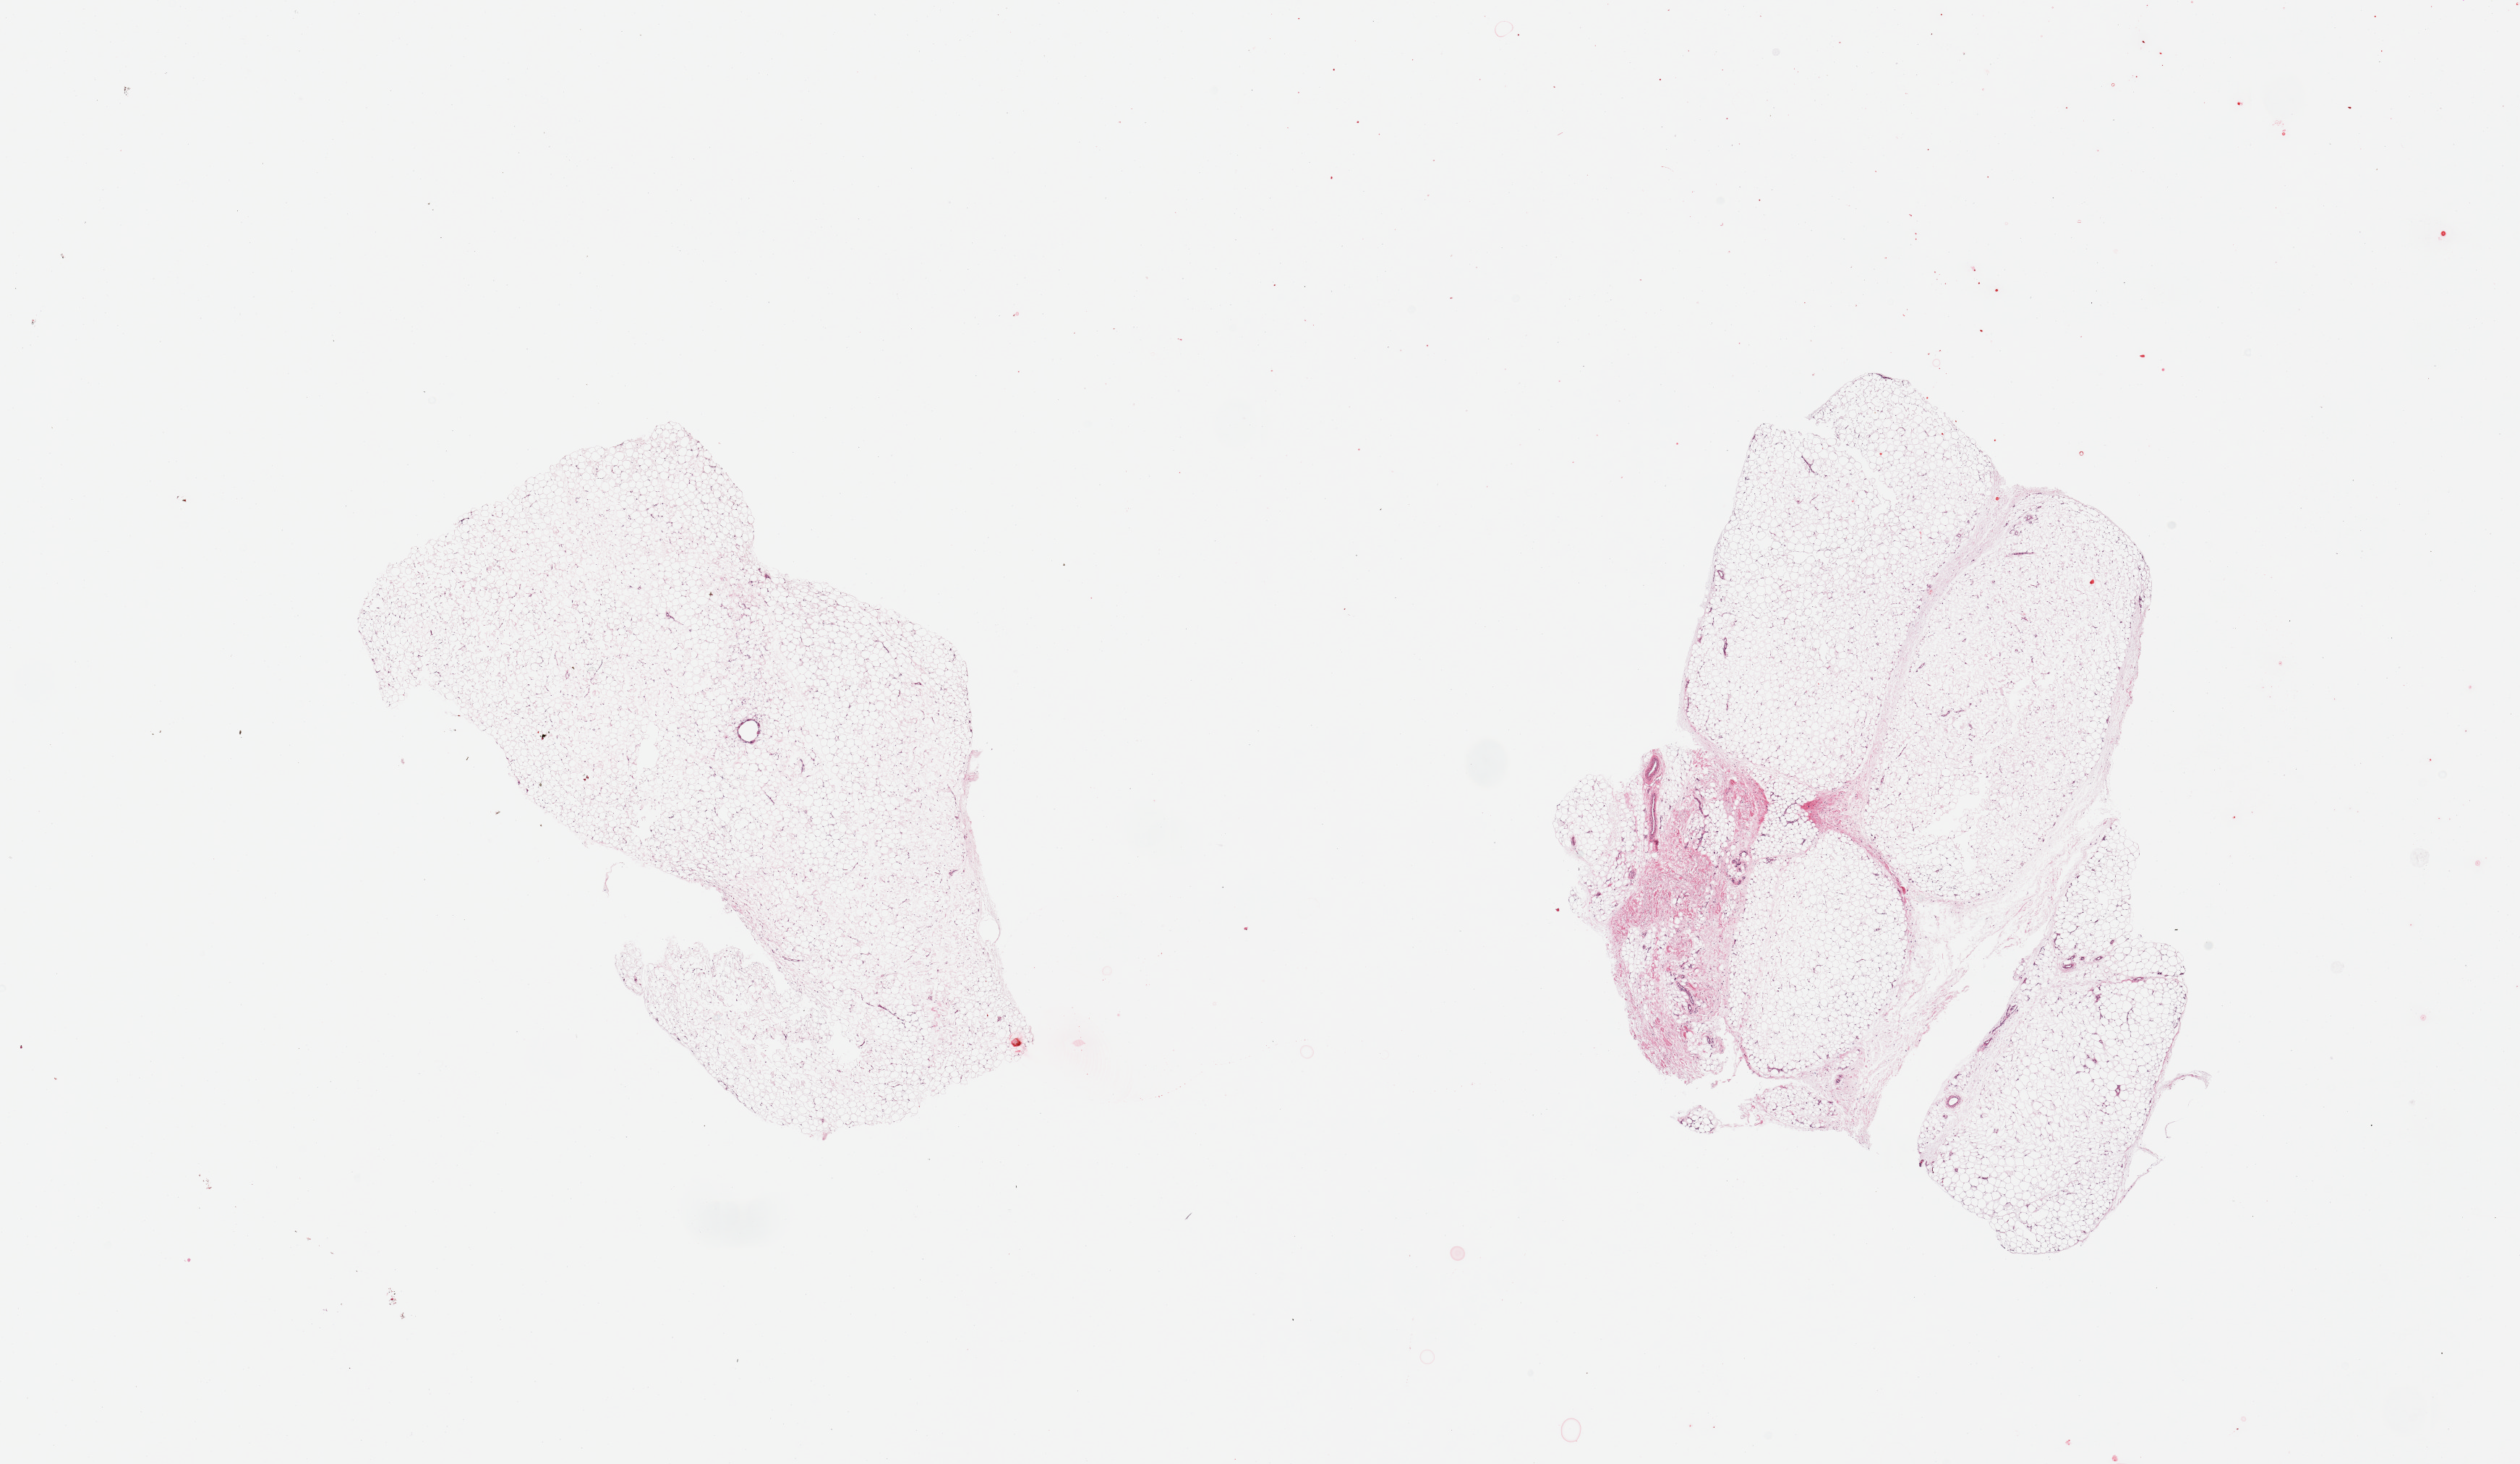
H&E whole-slide image — a low-resolution overview of the entire scanned area, about 27.6 x 16.0 mm. PAXgene-fixed paraffin-embedded (PFPE) section. Sampled site (target tissue): adipose tissue. Tissue donor sample. Male donor.
• review note (as recorded): 2 pieces